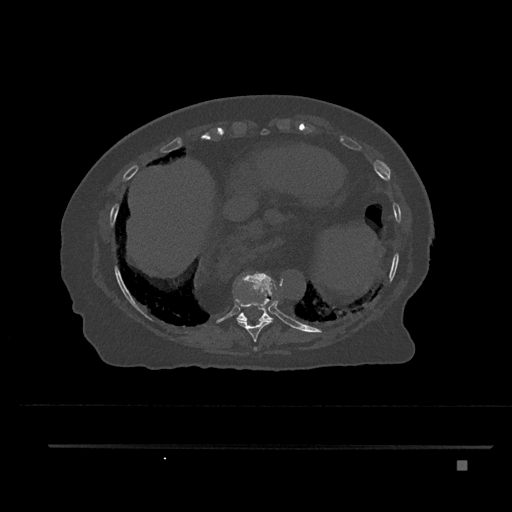
CT including the spine, one axial slice; slice 381 of 797 in the series (ordered by position); bone window (W 1800 / L 400 HU); 0.5 mm slice thickness; 512 × 512 image matrix, field of view 437 × 437 mm. Female patient, age 76 years. Case-level facts recorded for this patient, not image findings: primary cancer: lung.
Outlined on this slice (semi-automatic segmentation, software-assisted and operator-edited):
- T10 vertebra: bounding box [x1, y1, x2, y2] px = [236, 273, 274, 322]
- T8 vertebra: [254, 347, 257, 351]
- T9 vertebra: [234, 272, 273, 342]